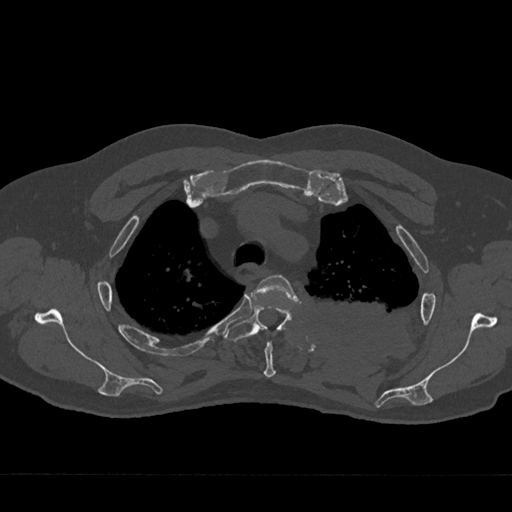
CT including the spine, one axial slice; position 541 of 797 along the scan axis; 120 kVp; bone window (W 1800 / L 400 HU); 0.5 mm slice thickness; 512 × 512 image matrix, field of view 377 × 377 mm. Patient: male, 75 years. From the clinical record (not read from this slice): primary cancer: renal; vertebrae with lytic lesions (as recorded): T4.
Annotated regions visible in this slice (semi-automatic segmentation, software-assisted and operator-edited):
- T3 vertebra: bounding box <251,275,297,378> (left, top, right, bottom; pixels)
- T4 vertebra: <225,304,292,342>